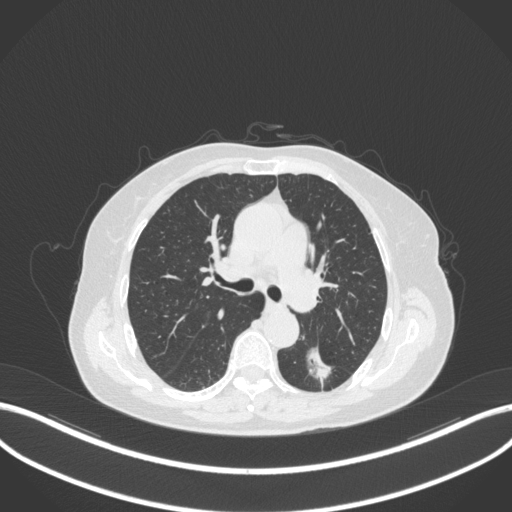
Chest CT, one axial slice. Slice 187 of 352 in the series (ordered by position). Reconstruction kernel B31f. 120 kVp. Lung window (W 1500 / L -600 HU). 1 mm slice thickness. 512 × 512 image matrix, field of view 400 × 400 mm. Patient: female, 70 years. From the clinical record (not read from this slice): clinical TNM (as recorded): T1c N0 M0.
Annotated regions visible in this slice (bounding box drawn by a radiologist):
- lung tumour (recorded histology: adenocarcinoma): bounding box (x1, y1, x2, y2) in pixels: (300, 339, 340, 391)